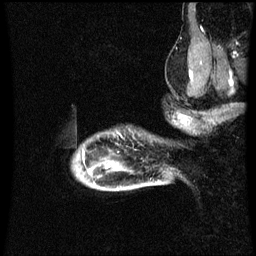
Breast MRI (dynamic contrast-enhanced), one sagittal slice; position 55 of 60 along the scan axis; dynamic contrast-enhanced series, image 2 of 3 at this slice position (ordered by acquisition); 1.5 T; TE 4.2 ms, TR 8.9 ms; 2 mm slice thickness; 256 × 256 image matrix, field of view 200 × 200 mm. Patient: female, 49 years. Case-level facts recorded for this patient, not image findings: setting: breast cancer imaged before/during neoadjuvant chemotherapy; receptor status: HR-positive, HER2-negative.
Outlined on this slice (semi-automatically segmented with operator editing):
- analysis volume of interest (the breast-tissue region the enhancement analysis was run in; not a lesion): bounding box [x1, y1, x2, y2] px = [74, 134, 159, 191]
- tumour enhancement mask (voxels above the 70 % enhancement threshold inside the analysis volume of interest): [88, 168, 93, 175]